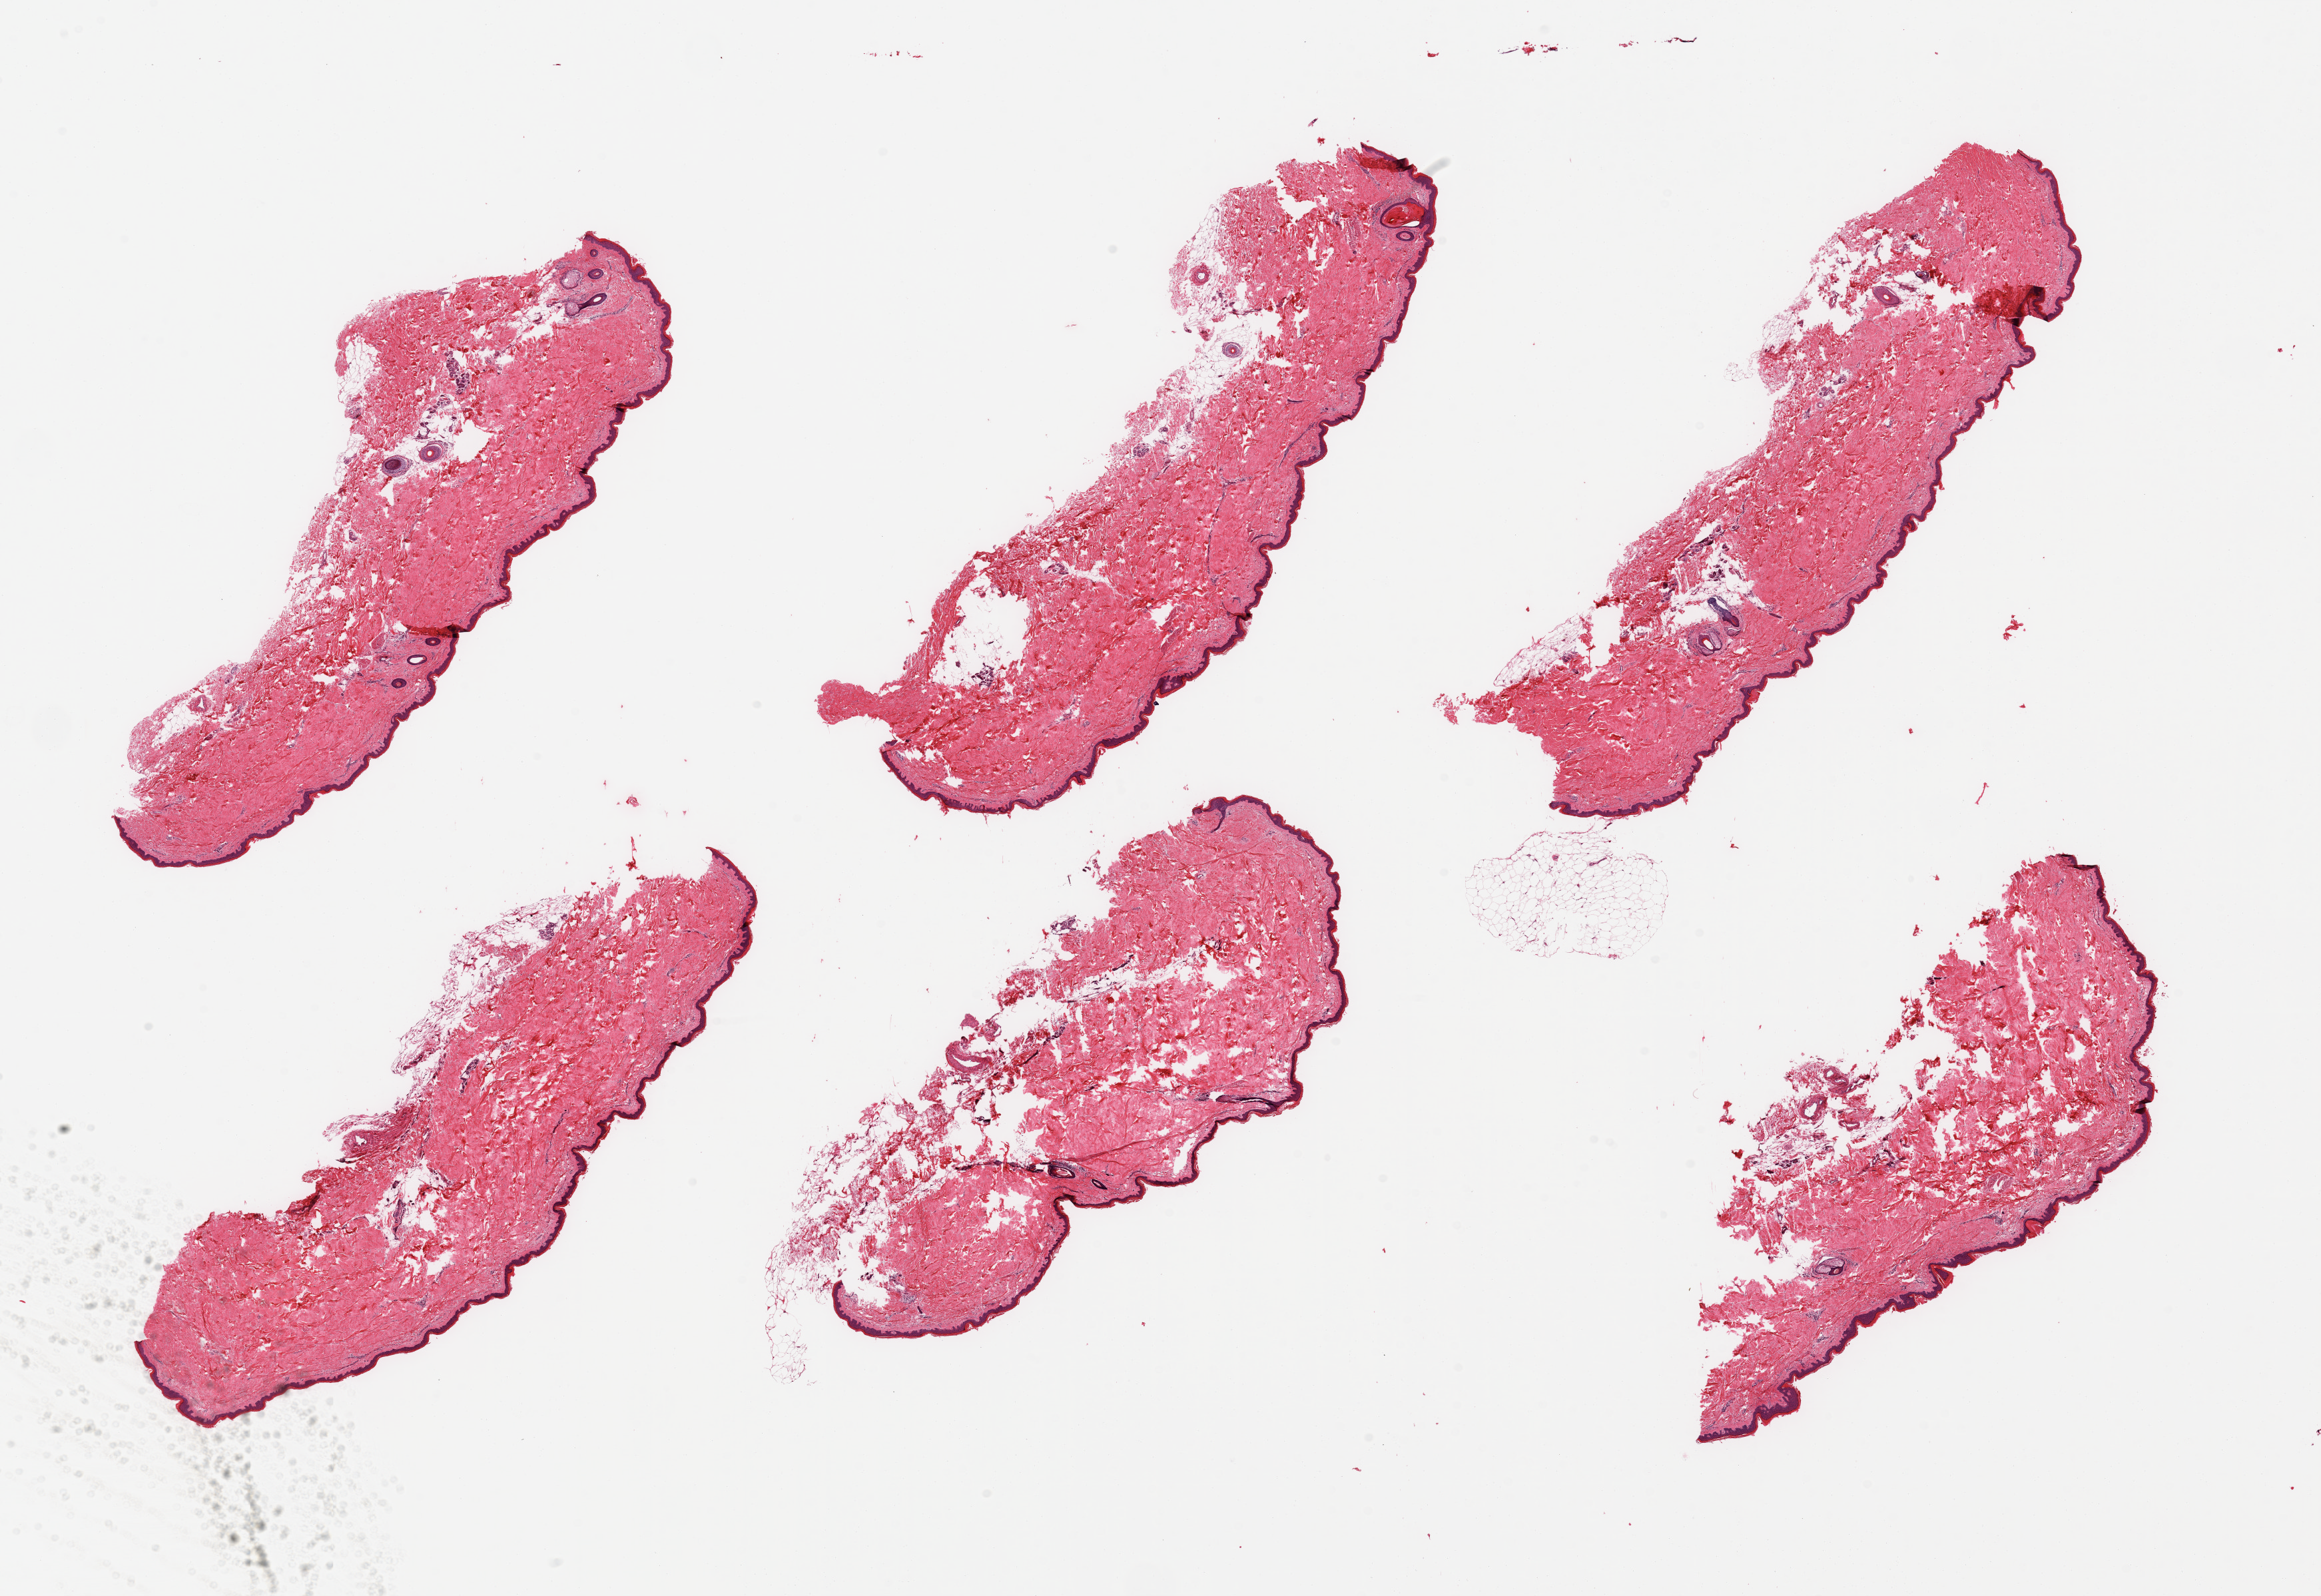
Digitized hematoxylin and eosin (H&E)-stained section, a low-resolution overview of the entire scanned area, about 27.6 x 19.0 mm (acquisition: 20x scan); PAXgene-fixed paraffin-embedded (PFPE) section; sampled site (target tissue): skin of lower leg; donor tissue sample.
Pathologist's review note for this sample: 6 pieces; include up to 10% internal/external fat, epidermis measures 45 microns, some sections fragmented.